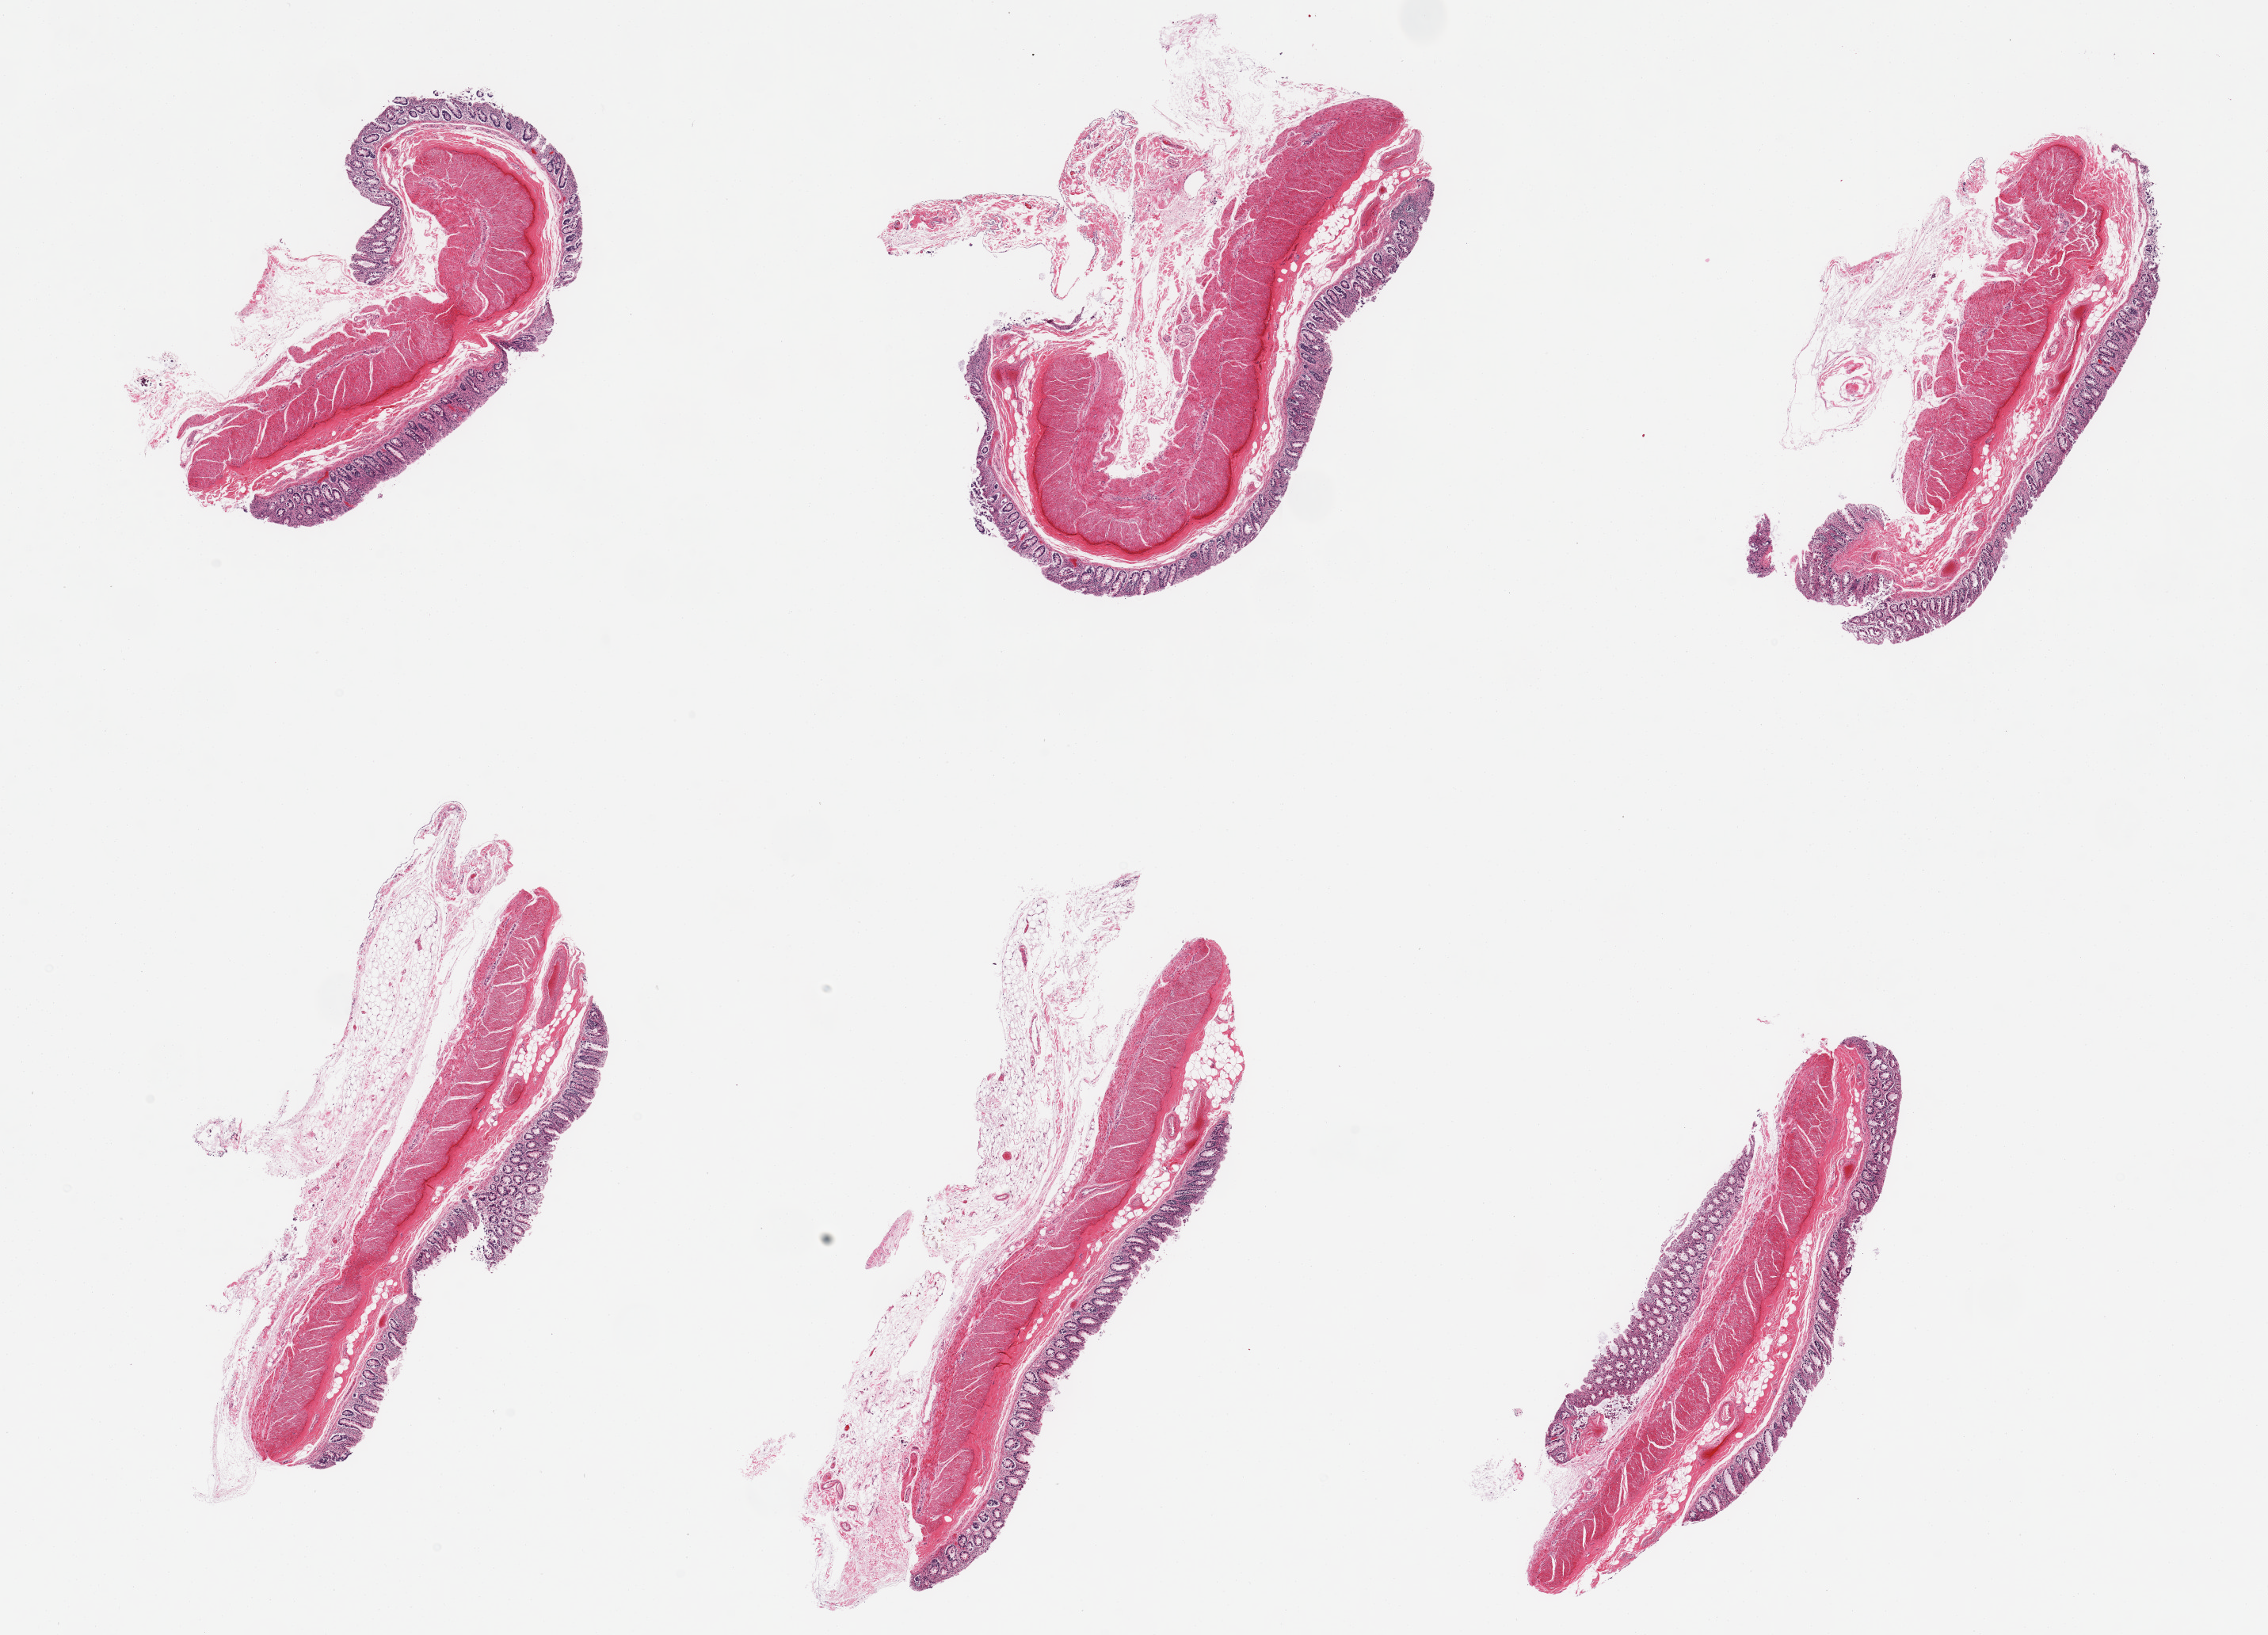
Digitized hematoxylin and eosin (H&E)-stained section — whole scanned area (about 22.6 x 16.3 mm, acquisition: 20x scan) shown as a low-resolution overview; PAXgene-fixed paraffin-embedded (PFPE) section; section of transverse colon (target tissue); donor tissue sample. Donor sex: male.
Review note (as recorded): 6 pieces, mucosa up to ~0.3mm, autolysis advanced, partially sloughed.